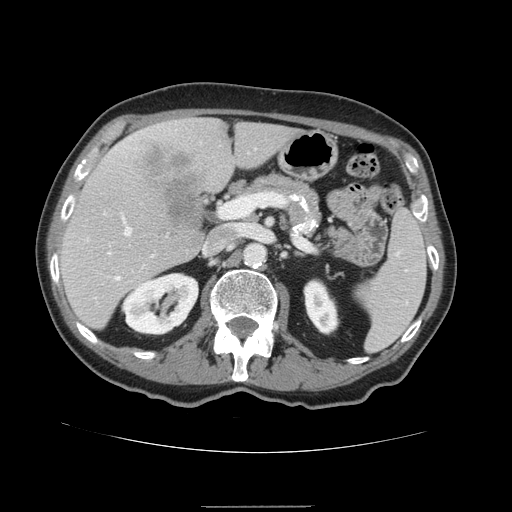
Contrast-enhanced abdominal CT, one axial slice; slice 83 of 168 in the series (ordered by position); 120 kVp; soft-tissue window (W 400 / L 40 HU); 512 × 512 image matrix. Male patient, age 74 years. Case-level facts recorded for this patient, not image findings: diagnosis: colorectal cancer liver metastases, imaged before liver resection; multiple liver metastases: no; largest metastasis: 14.5 cm; disease in both lobes: yes.
Annotated regions visible in this slice (outlined manually by an expert reader):
- hepatic veins: bounding box (x1, y1, x2, y2) in pixels: (117, 218, 132, 279)
- liver: (60, 117, 302, 330)
- planned liver remnant (the part of the liver to remain after resection): (60, 122, 301, 331)
- portal vein (with intrahepatic branches): (106, 200, 240, 269)
- liver metastasis: (136, 140, 212, 231)